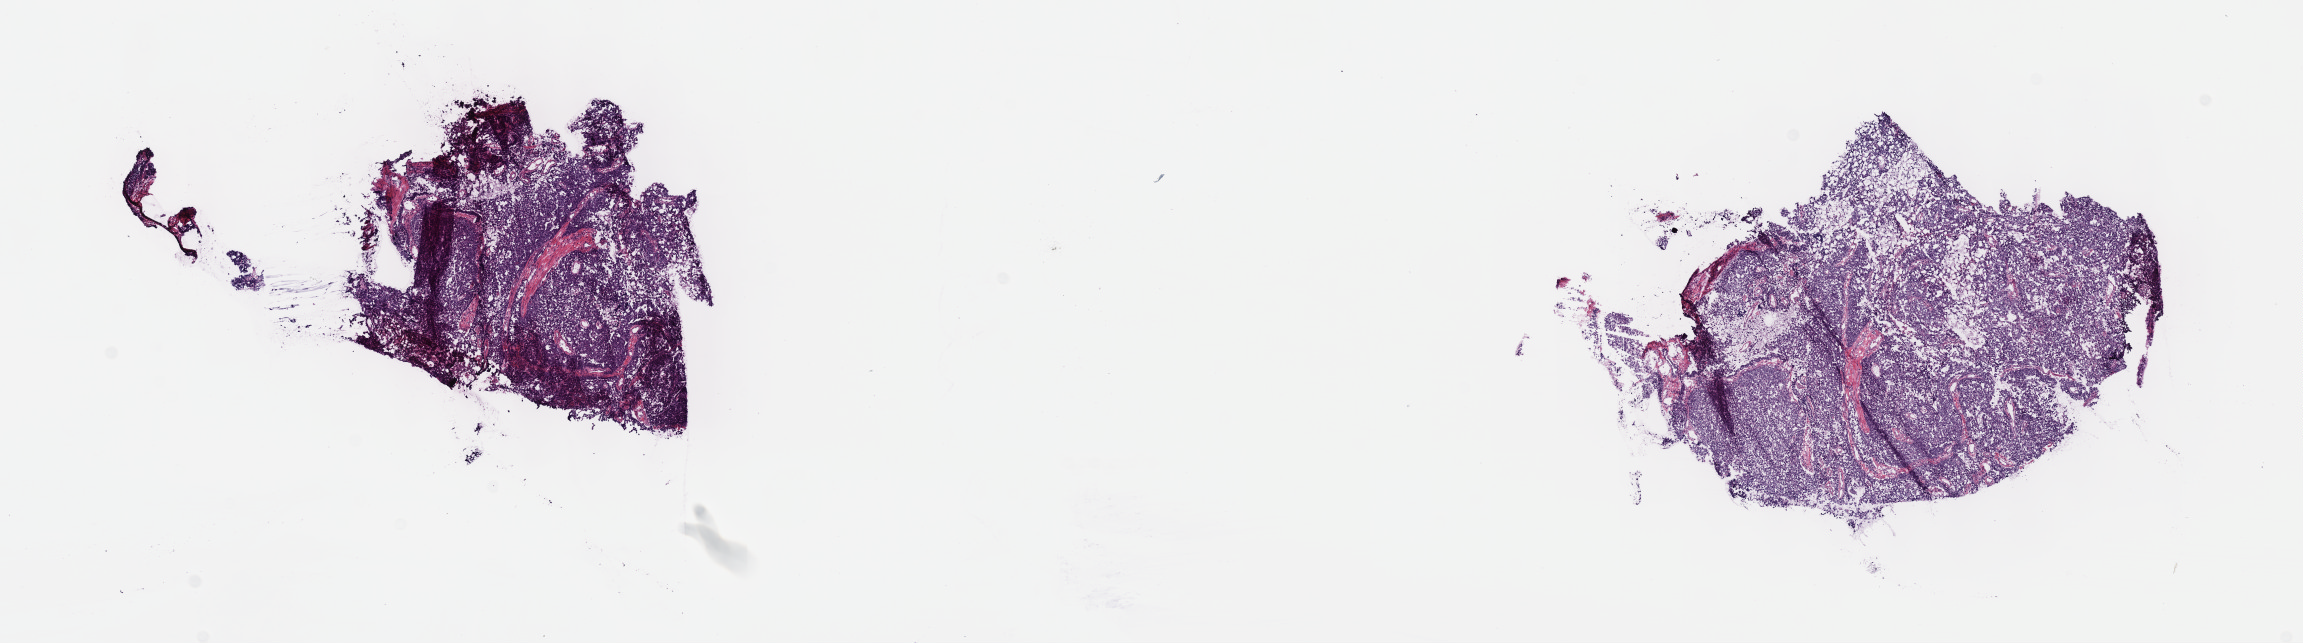
Whole-slide histology image, H&E, whole scanned area (about 18.6 x 5.2 mm, acquisition: 40x scan) shown as a low-resolution overview; frozen section; sample: primary tumour, ovary. Female patient; age at initial diagnosis 72 years. Histologic grade: G3 (poorly differentiated). Pathologist review of this section (percent, as recorded): tumour cells 85%, tumour nuclei 90%, normal cells 0%, stromal cells 10%, necrosis 5%. Inflammatory infiltration, as recorded: lymphocyte infiltration 0%, monocyte infiltration 0%, neutrophil infiltration 0%.
FIGO stage: IIIC. Diagnosis: Serous cystadenocarcinoma, NOS.